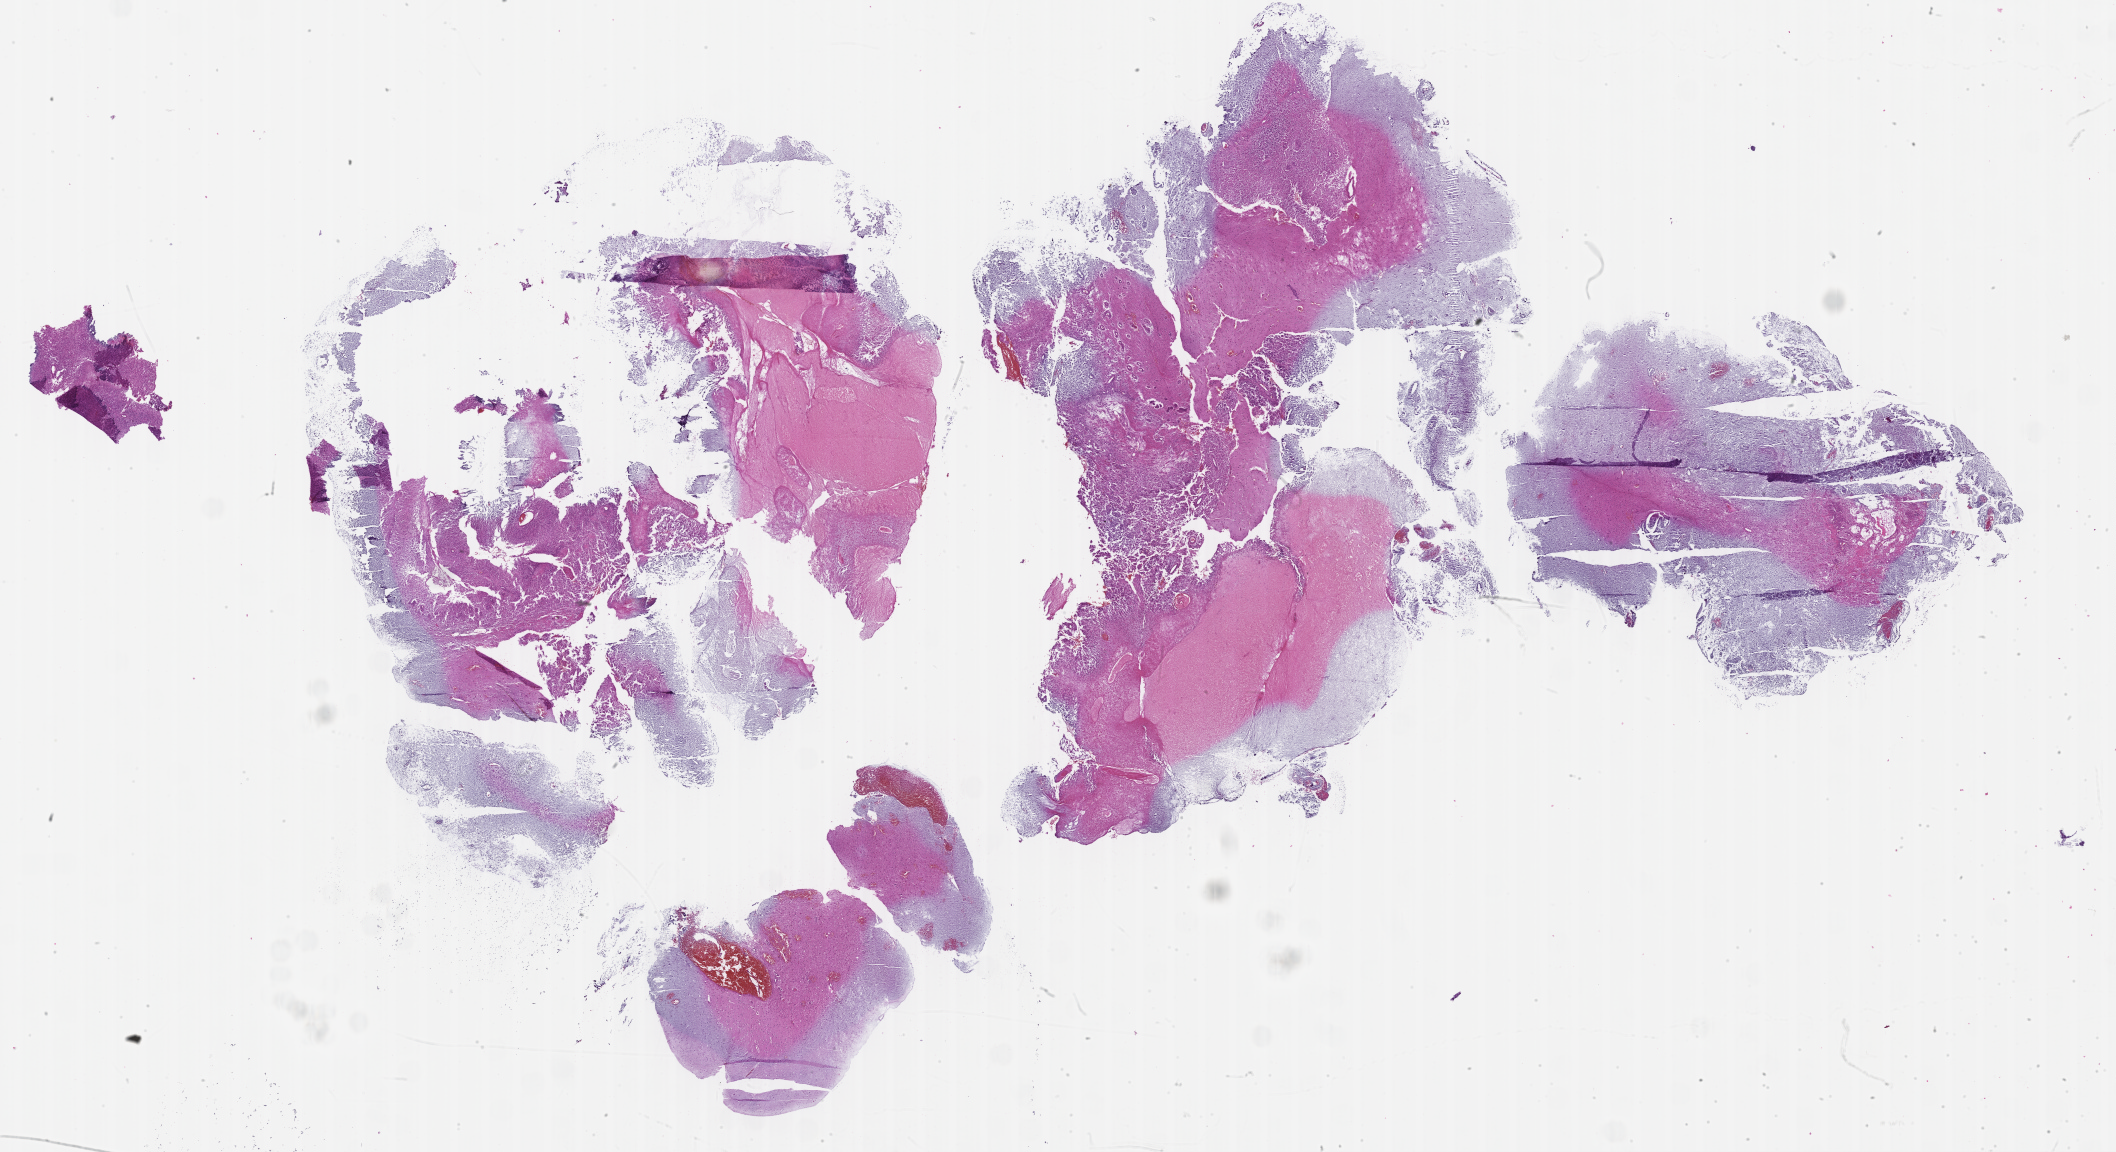
Whole-slide histology image, Hematoxylin and eosin (H&E) stained, low-resolution overview of the scanned area, about 34.3 x 18.7 mm (from a 40x scan); formalin-fixed paraffin-embedded (FFPE) diagnostic section; primary tumour sample from the brain. Patient: male, age at initial diagnosis 48 years.
- pathologic diagnosis: Glioblastoma